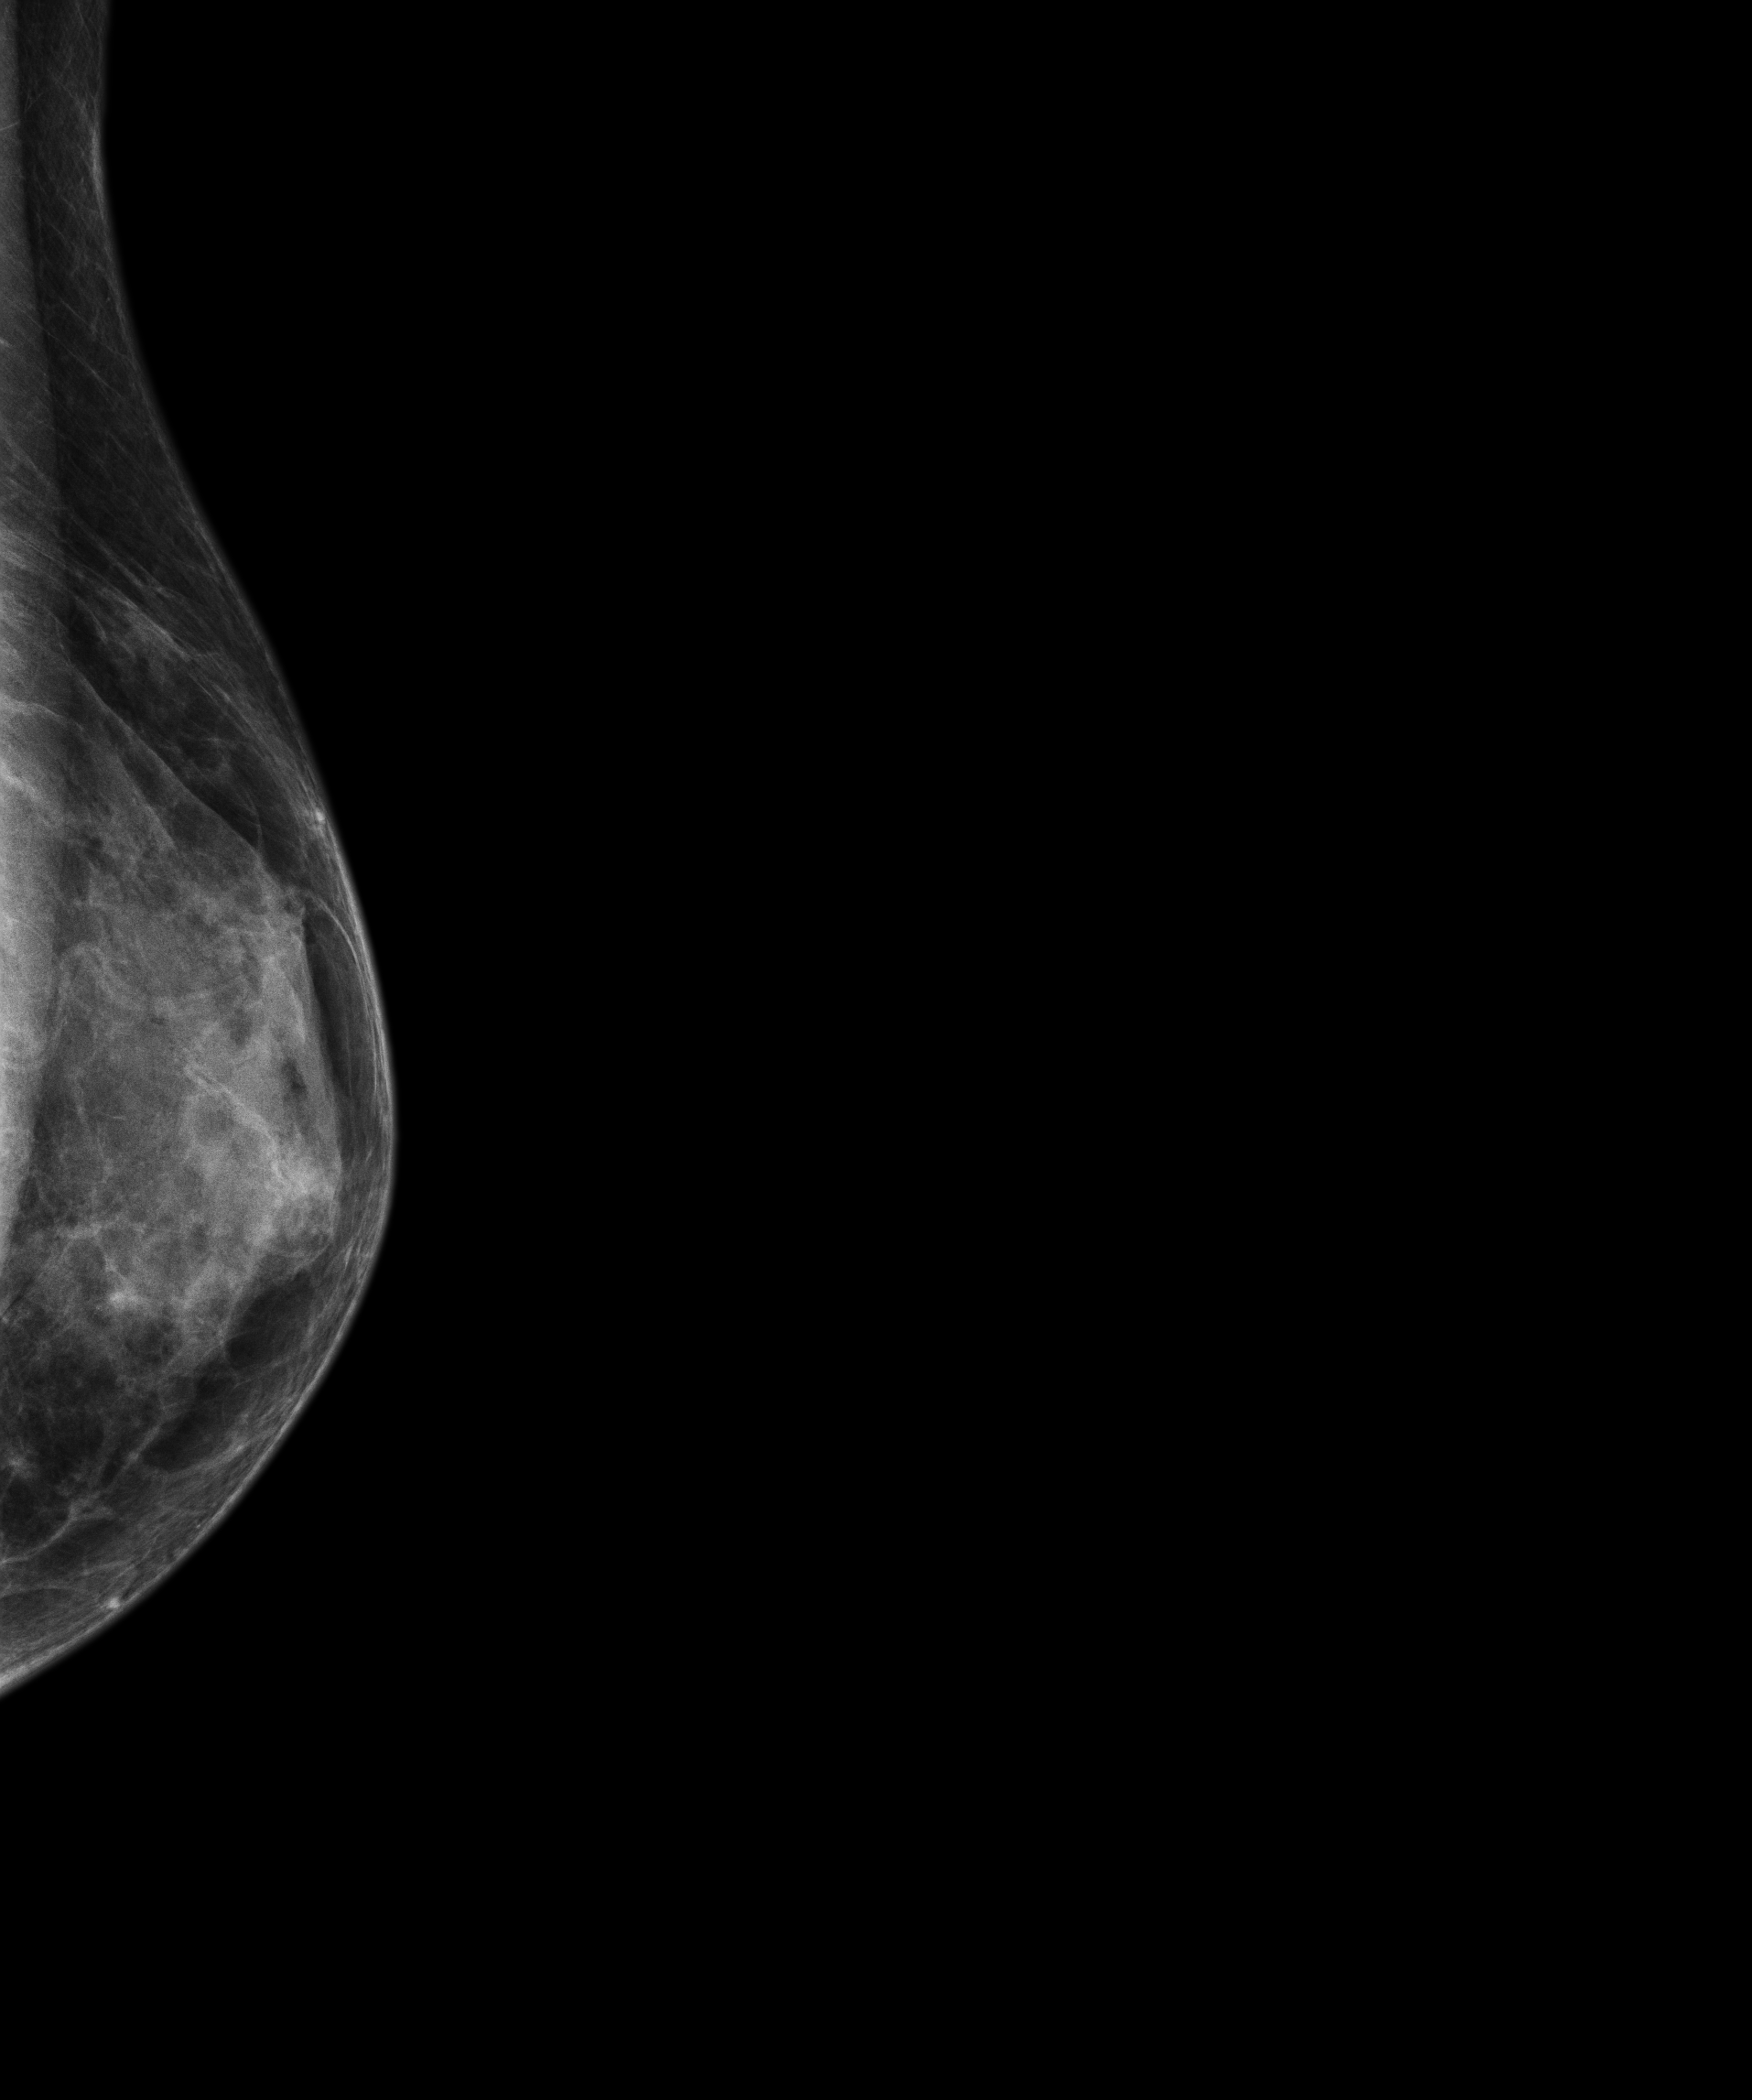
Annual screening mammography examination; compressed breast thickness 29 mm; system: Senographe Essential ADS_56.21.3. Female patient, age 56 years.
Image type: full-field digital mammogram. Breast: left. Projection: laterally exaggerated craniocaudal (XCCL) view.